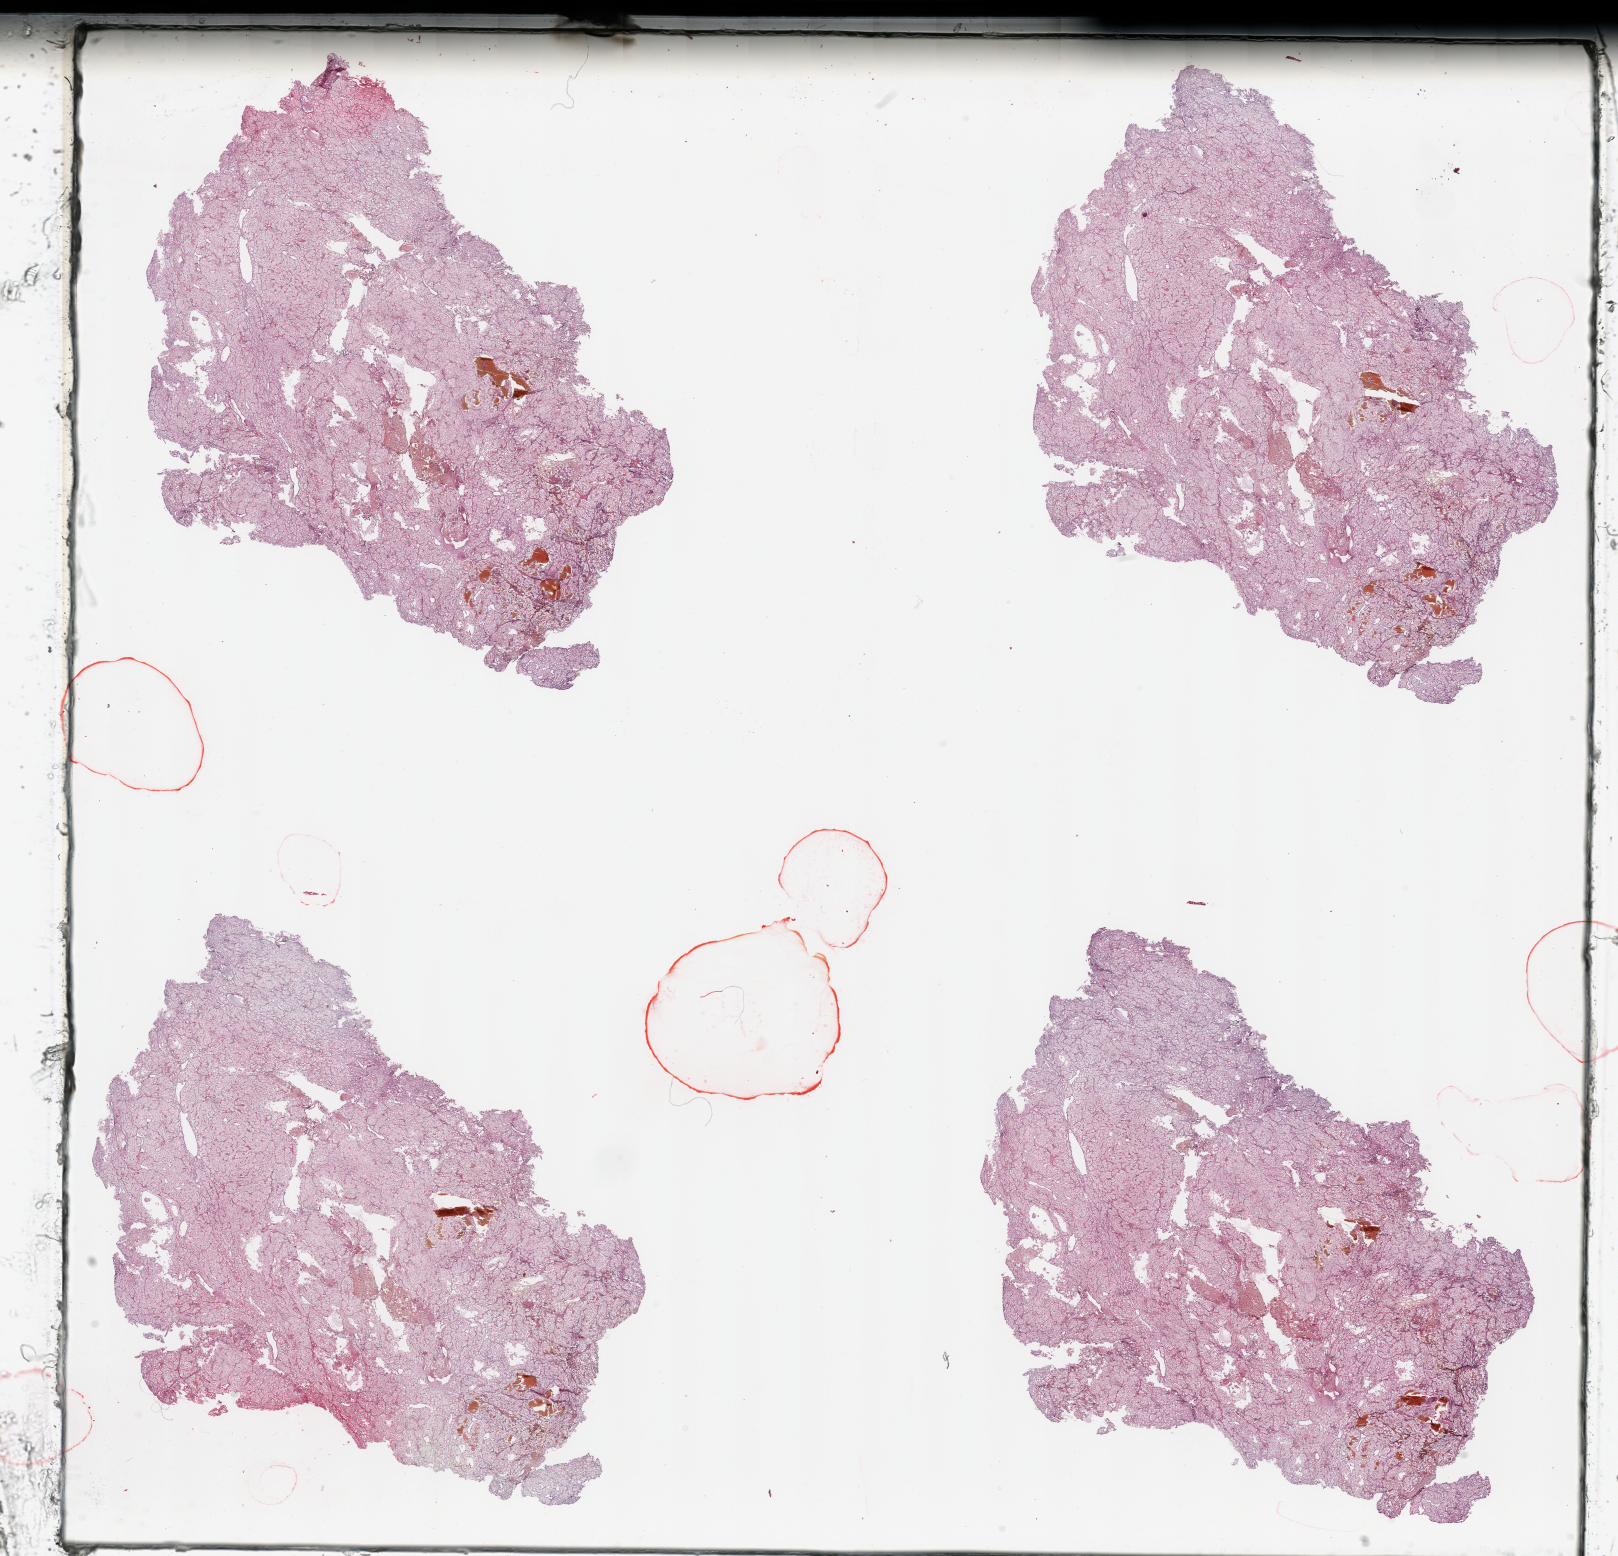
Hematoxylin and eosin (H&E) stained whole-slide image — shown as a low-resolution overview of the whole scanned area (about 25.6 x 24.6 mm, from a 20x scan), tumour tissue sample, sampled site: kidney. Patient: female, age 86 years. Histologic grade: G3 (poorly differentiated). Pathologist review of this section (percent, as recorded): tumour nuclei 85%, necrosis 3%.
- diagnosis: Renal cell carcinoma, NOS
- primary tumour site (as recorded): upper pole
- AJCC pathologic stage: IV